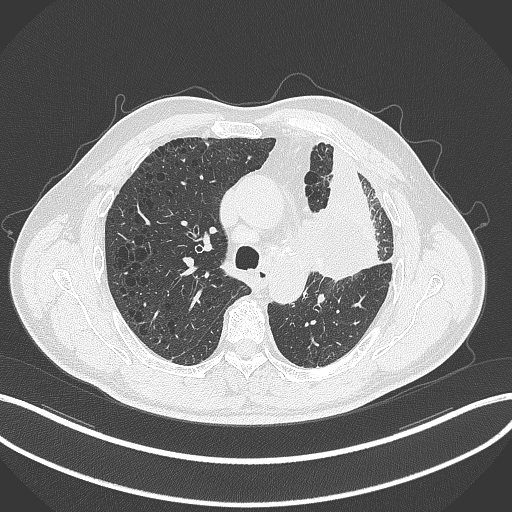
Chest CT, one axial slice; position 211 of 297 along the scan axis; reconstruction kernel B70f; 120 kVp; lung window (W 1500 / L -600 HU); 1 mm slice thickness; 512 × 512 image matrix, field of view 400 × 400 mm. Male patient, age 68 years. From the clinical record (not read from this slice): clinical TNM (as recorded): T3 N3 M1.
Annotated regions visible in this slice (bounding box drawn by a radiologist):
- lung tumour (recorded histology: adenocarcinoma): bounding box (x1, y1, x2, y2) in pixels: (318, 194, 386, 282)